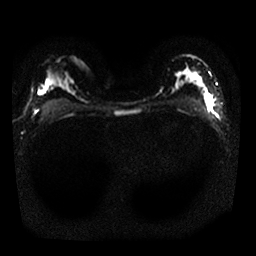
Breast MRI, one axial slice; slice 17 of 25 in the series (ordered by position); diffusion-weighted series; image 2 of 4 stored at this slice position (different b-values; order by instance number); 1.5 T; 4 mm slice thickness; 256 × 256 image matrix, field of view 320 × 320 mm. Female patient.
Structures marked on this image (expert manual segmentation):
- tumour on diffusion-weighted imaging: bounding box [x1, y1, x2, y2] px = [197, 73, 213, 106]